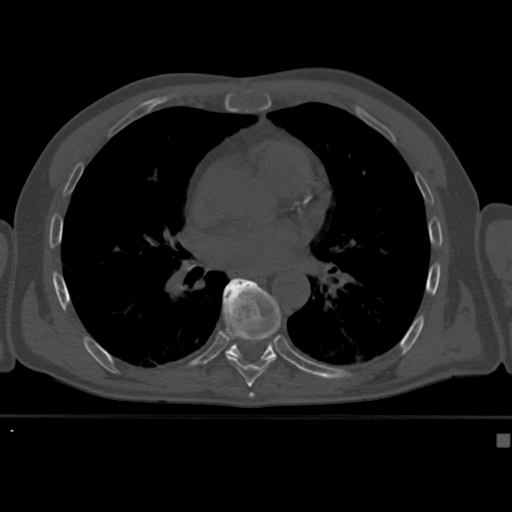
CT including the spine, one axial slice. Position 257 of 430 along the scan axis. Reconstruction kernel Br40s. 120 kVp. Bone window (W 1800 / L 400 HU). 1.5 mm slice thickness. 512 × 512 image matrix, field of view 337 × 337 mm. Male patient, age 64 years. Case-level facts recorded for this patient, not image findings: primary cancer: uterus.
Annotated regions visible in this slice (semi-automatic segmentation, software-assisted and operator-edited):
- T8 vertebra: bounding box (x1, y1, x2, y2) in pixels: (220, 281, 282, 382)
- T9 vertebra: (223, 278, 282, 365)